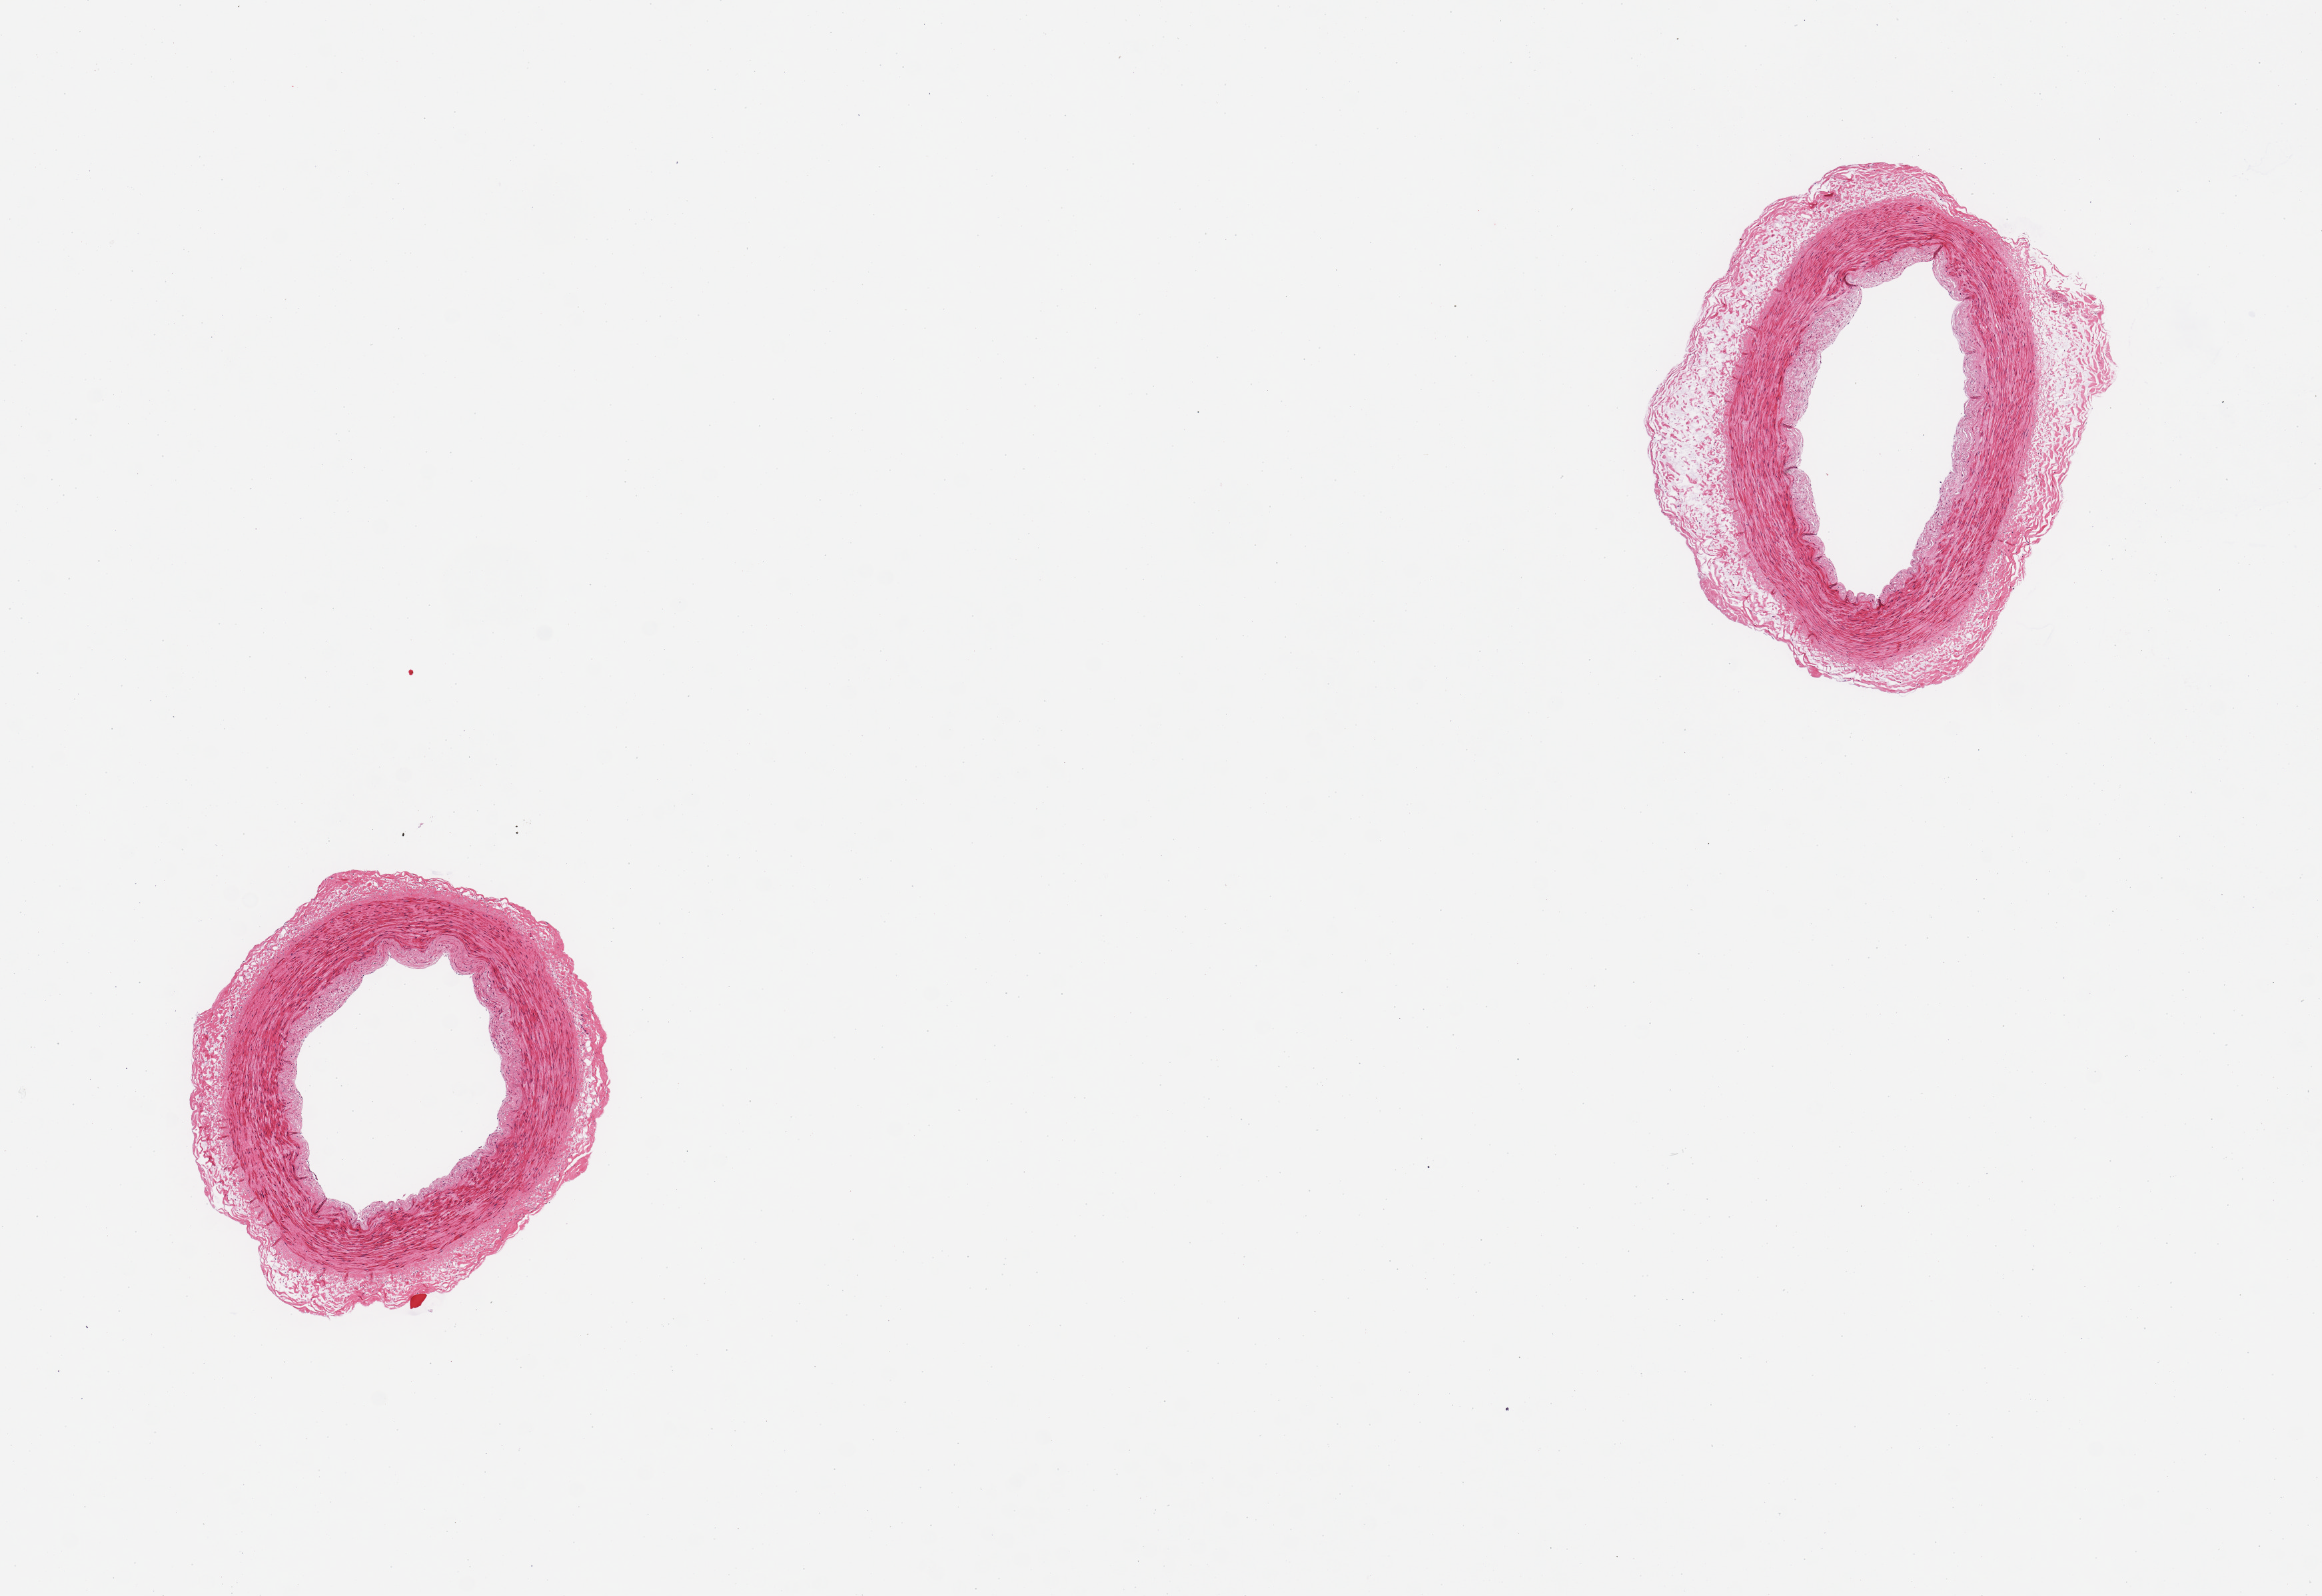
Hematoxylin and eosin (H&E) whole-slide image, whole scanned area (about 13.8 x 9.5 mm, acquisition: 20x scan) shown as a low-resolution overview, PAXgene-fixed paraffin-embedded (PFPE) section, sampled site (target tissue): tibial artery, donor tissue sample. Donor sex: male.
Review note (as recorded): 2 pieces, trace rim of adherent fibradipose tissue up to ~0.5mm.